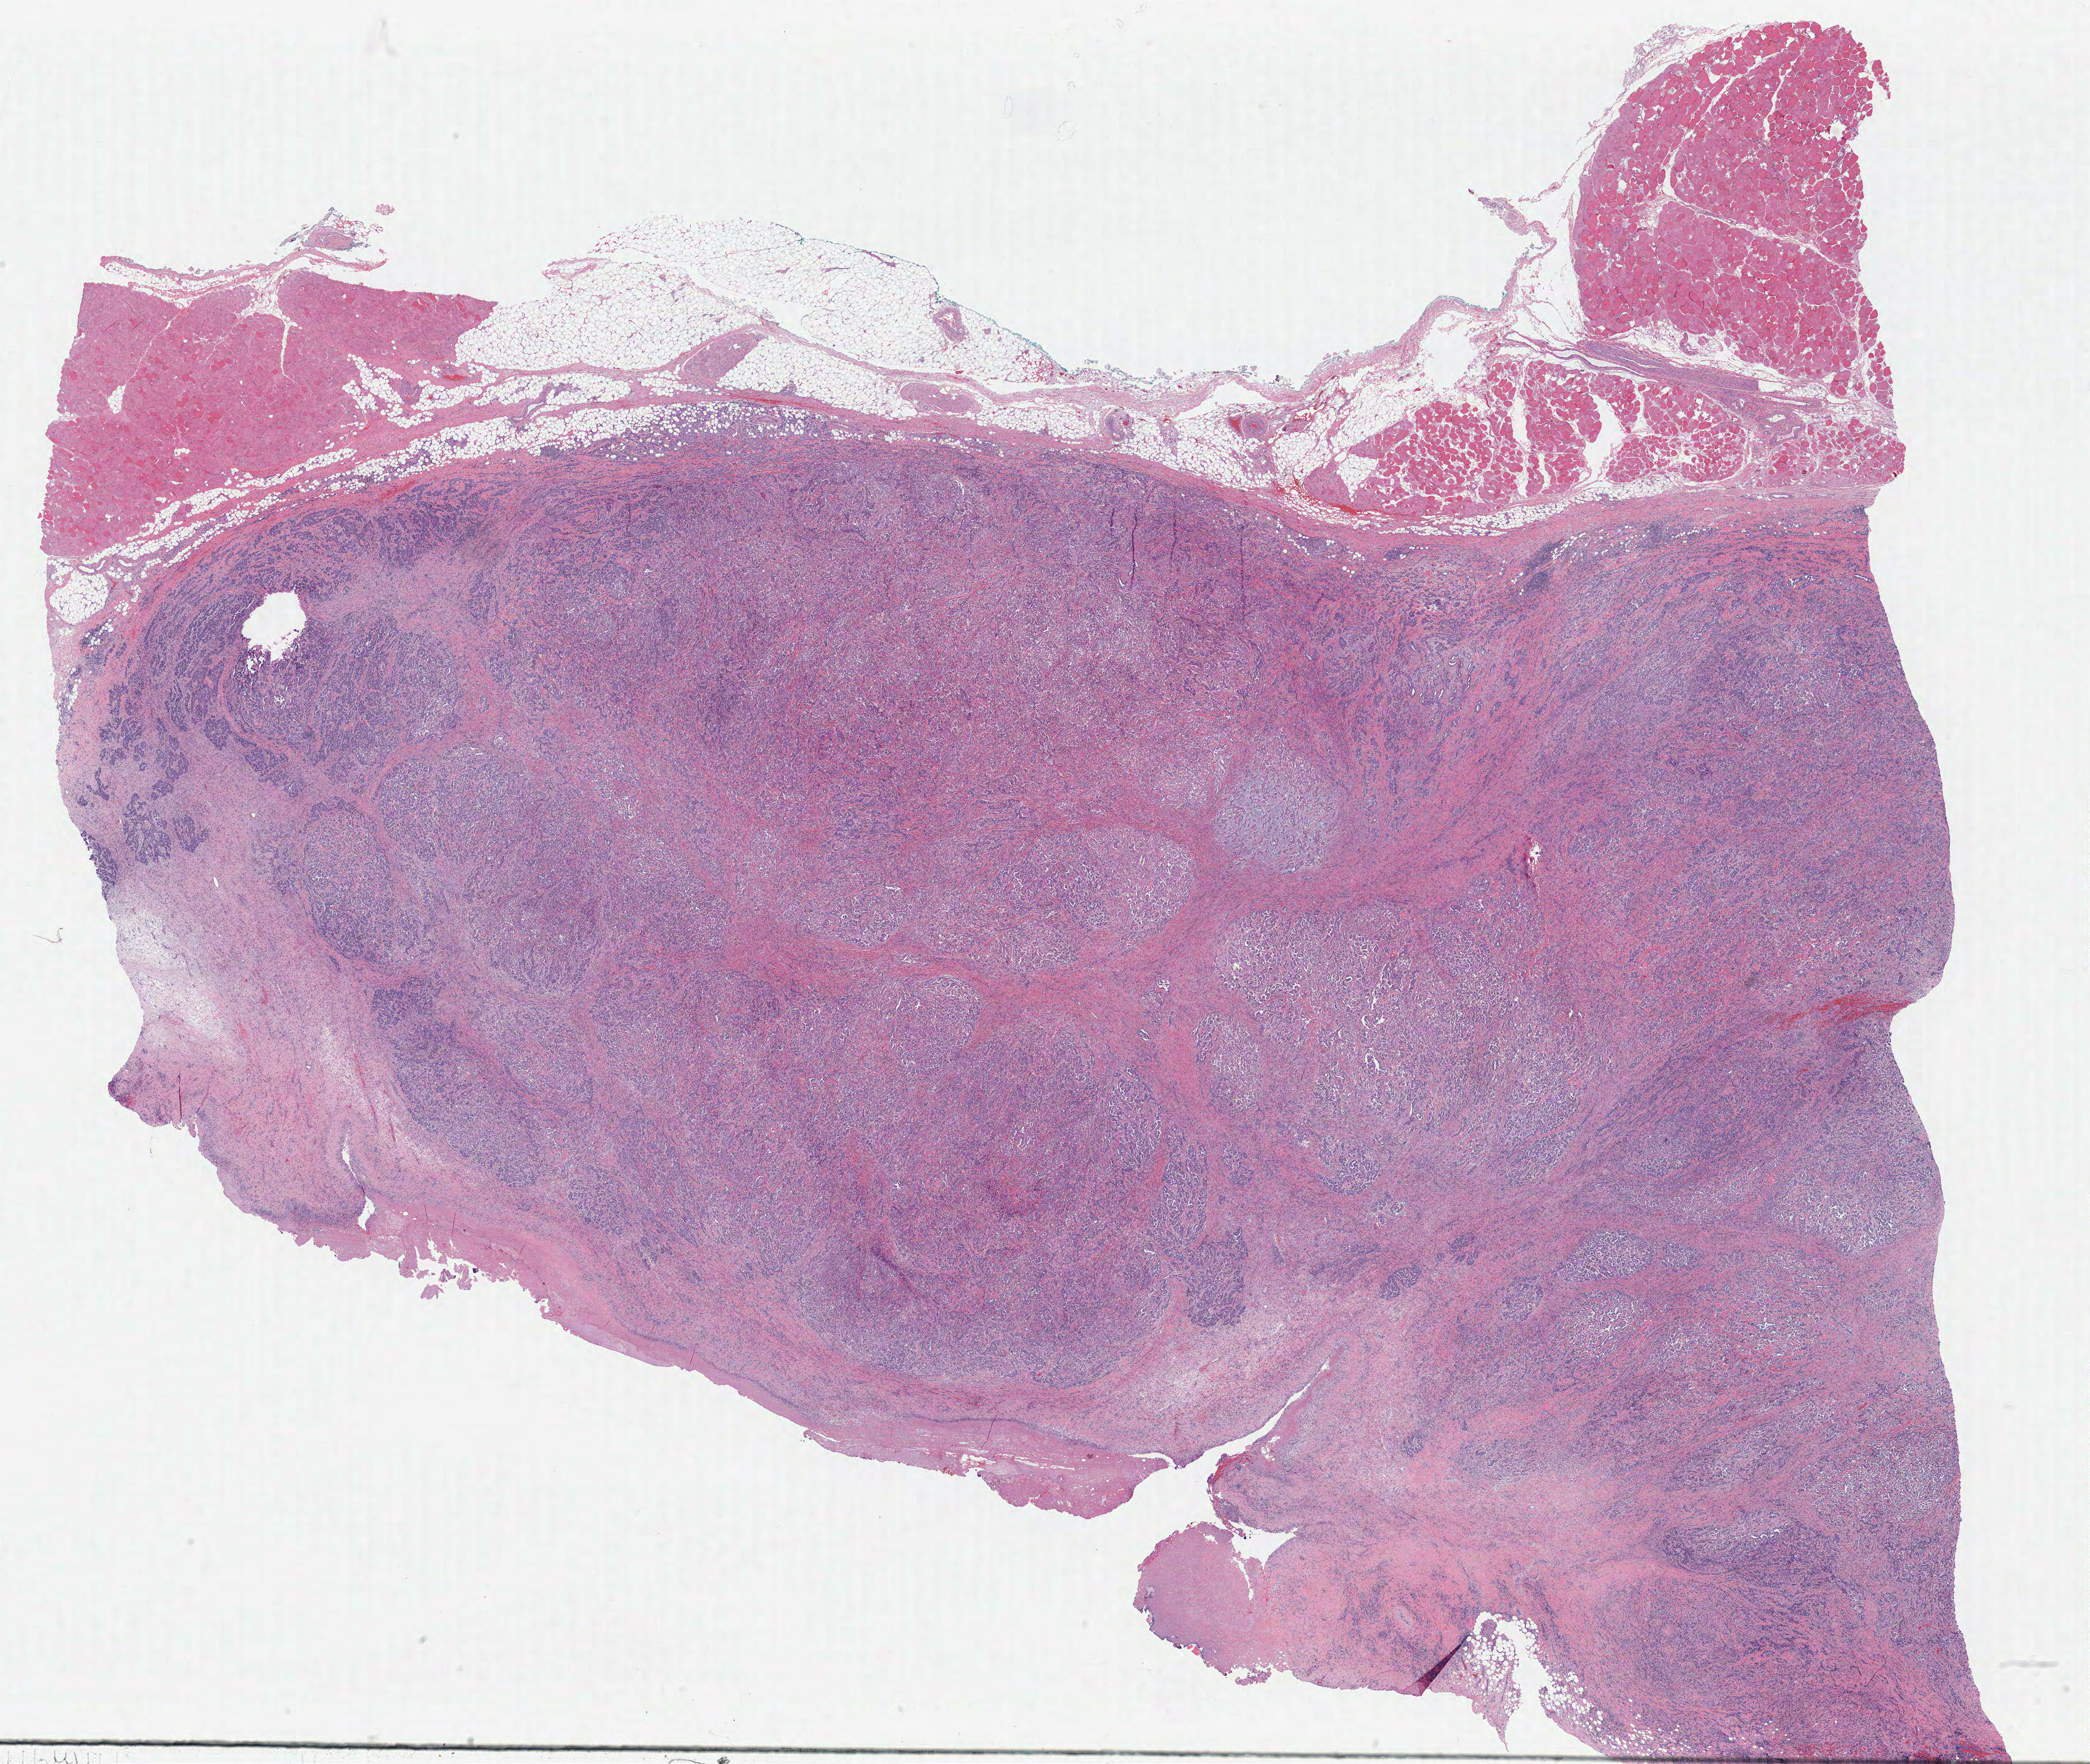
H&E whole-slide image — a low-resolution overview of the entire scanned area, about 27.1 x 22.8 mm, formalin-fixed paraffin-embedded (FFPE) diagnostic section, primary tumour sample from the mesothelium. Patient: male, age at initial diagnosis 55 years.
- AJCC pathologic stage: III (7th edition)
- pathologic diagnosis: Epithelioid mesothelioma, malignant (pleura, NOS)